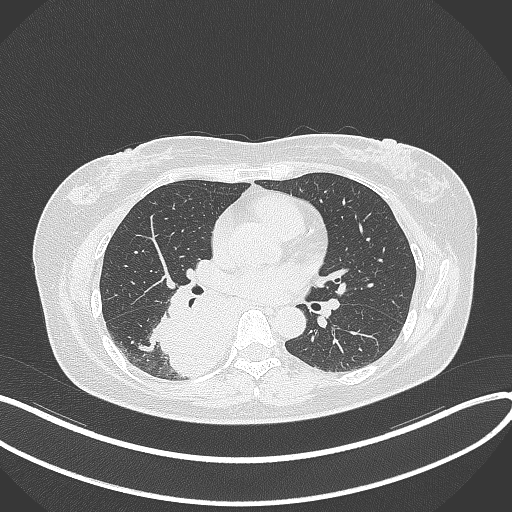
Chest CT, one axial slice; position 184 of 331 along the scan axis; 120 kVp; lung window (W 1500 / L -600 HU); 512 × 512 image matrix, field of view 400 × 400 mm. Patient: female, 54 years. From the clinical record (not read from this slice): clinical TNM (as recorded): T4 N0 M0.
Structures marked on this image (rectangle marked by the reading radiologist):
- lung tumour (recorded histology: adenocarcinoma): bounding box (x1, y1, x2, y2) in pixels: (155, 274, 234, 381)